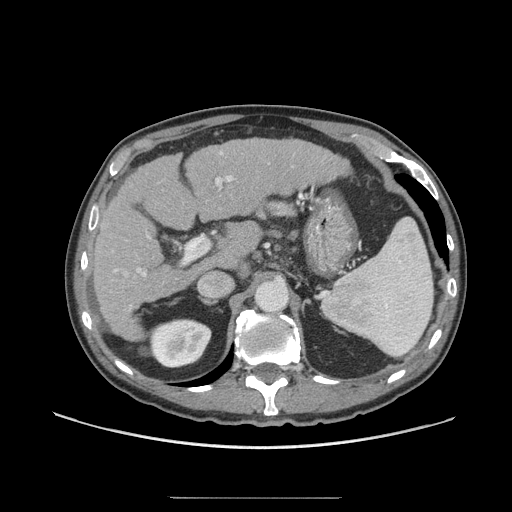
Contrast-enhanced abdominal CT (liver protocol), one axial slice; position 40 of 71 along the scan axis; 140 kVp; soft-tissue window (W 400 / L 40 HU); 512 × 512 image matrix, field of view 400 × 400 mm. Case-level facts recorded for this patient, not image findings: diagnosis: hepatocellular carcinoma (patient treated with transarterial chemoembolisation; whether this scan precedes or follows treatment is not stated here); TNM stage (as recorded): Stage-I; Child-Pugh class: A; tumour differentiation: well differentiated; tumour nodularity: uninodular.
Outlined on this slice (semi-automatic segmentation, software-assisted and operator-edited):
- liver parenchyma outside the tumour (the mass and vessels are separate outlines, so this box may not span the whole liver): bounding box <92,138,348,340> (left, top, right, bottom; pixels)
- liver vessels: <113,152,234,277>